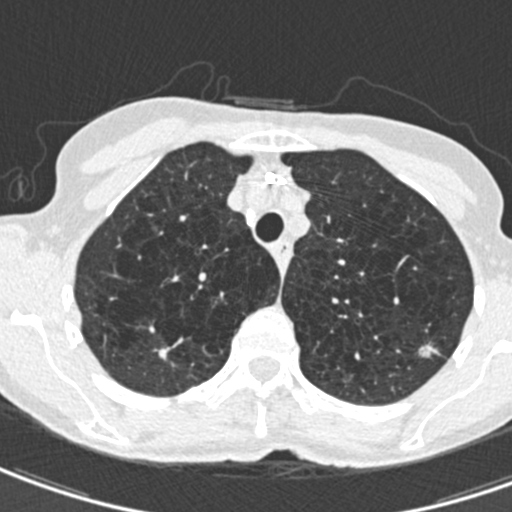
Low-dose screening chest CT, axial slice, second screening round (one year after baseline), lung window (W 1500 / L -600 HU), standard (soft-tissue) reconstruction kernel (B30f), 512 × 512 image matrix, field of view 272 × 272 mm. Female participant, aged 71 years at enrolment. Current smoker at enrolment.
Expert-annotated lung lesion, bounding box <404,331,444,369> (left, top, right, bottom; pixels). The screening reader recorded 2 non-calcified nodules or masses ≥4 mm on this exam; which of them this box marks is not recorded. Official screen result: positive, change unspecified: nodule(s) >= 4 mm or enlarging nodule(s), mass(es), or other non-specific abnormalities suspicious for lung cancer. Lung cancer was diagnosed 604 days after this screen: adenocarcinoma, NOS, left upper lobe, moderately differentiated (G2), stage IA (AJCC 6th edition), 12 mm at pathology.